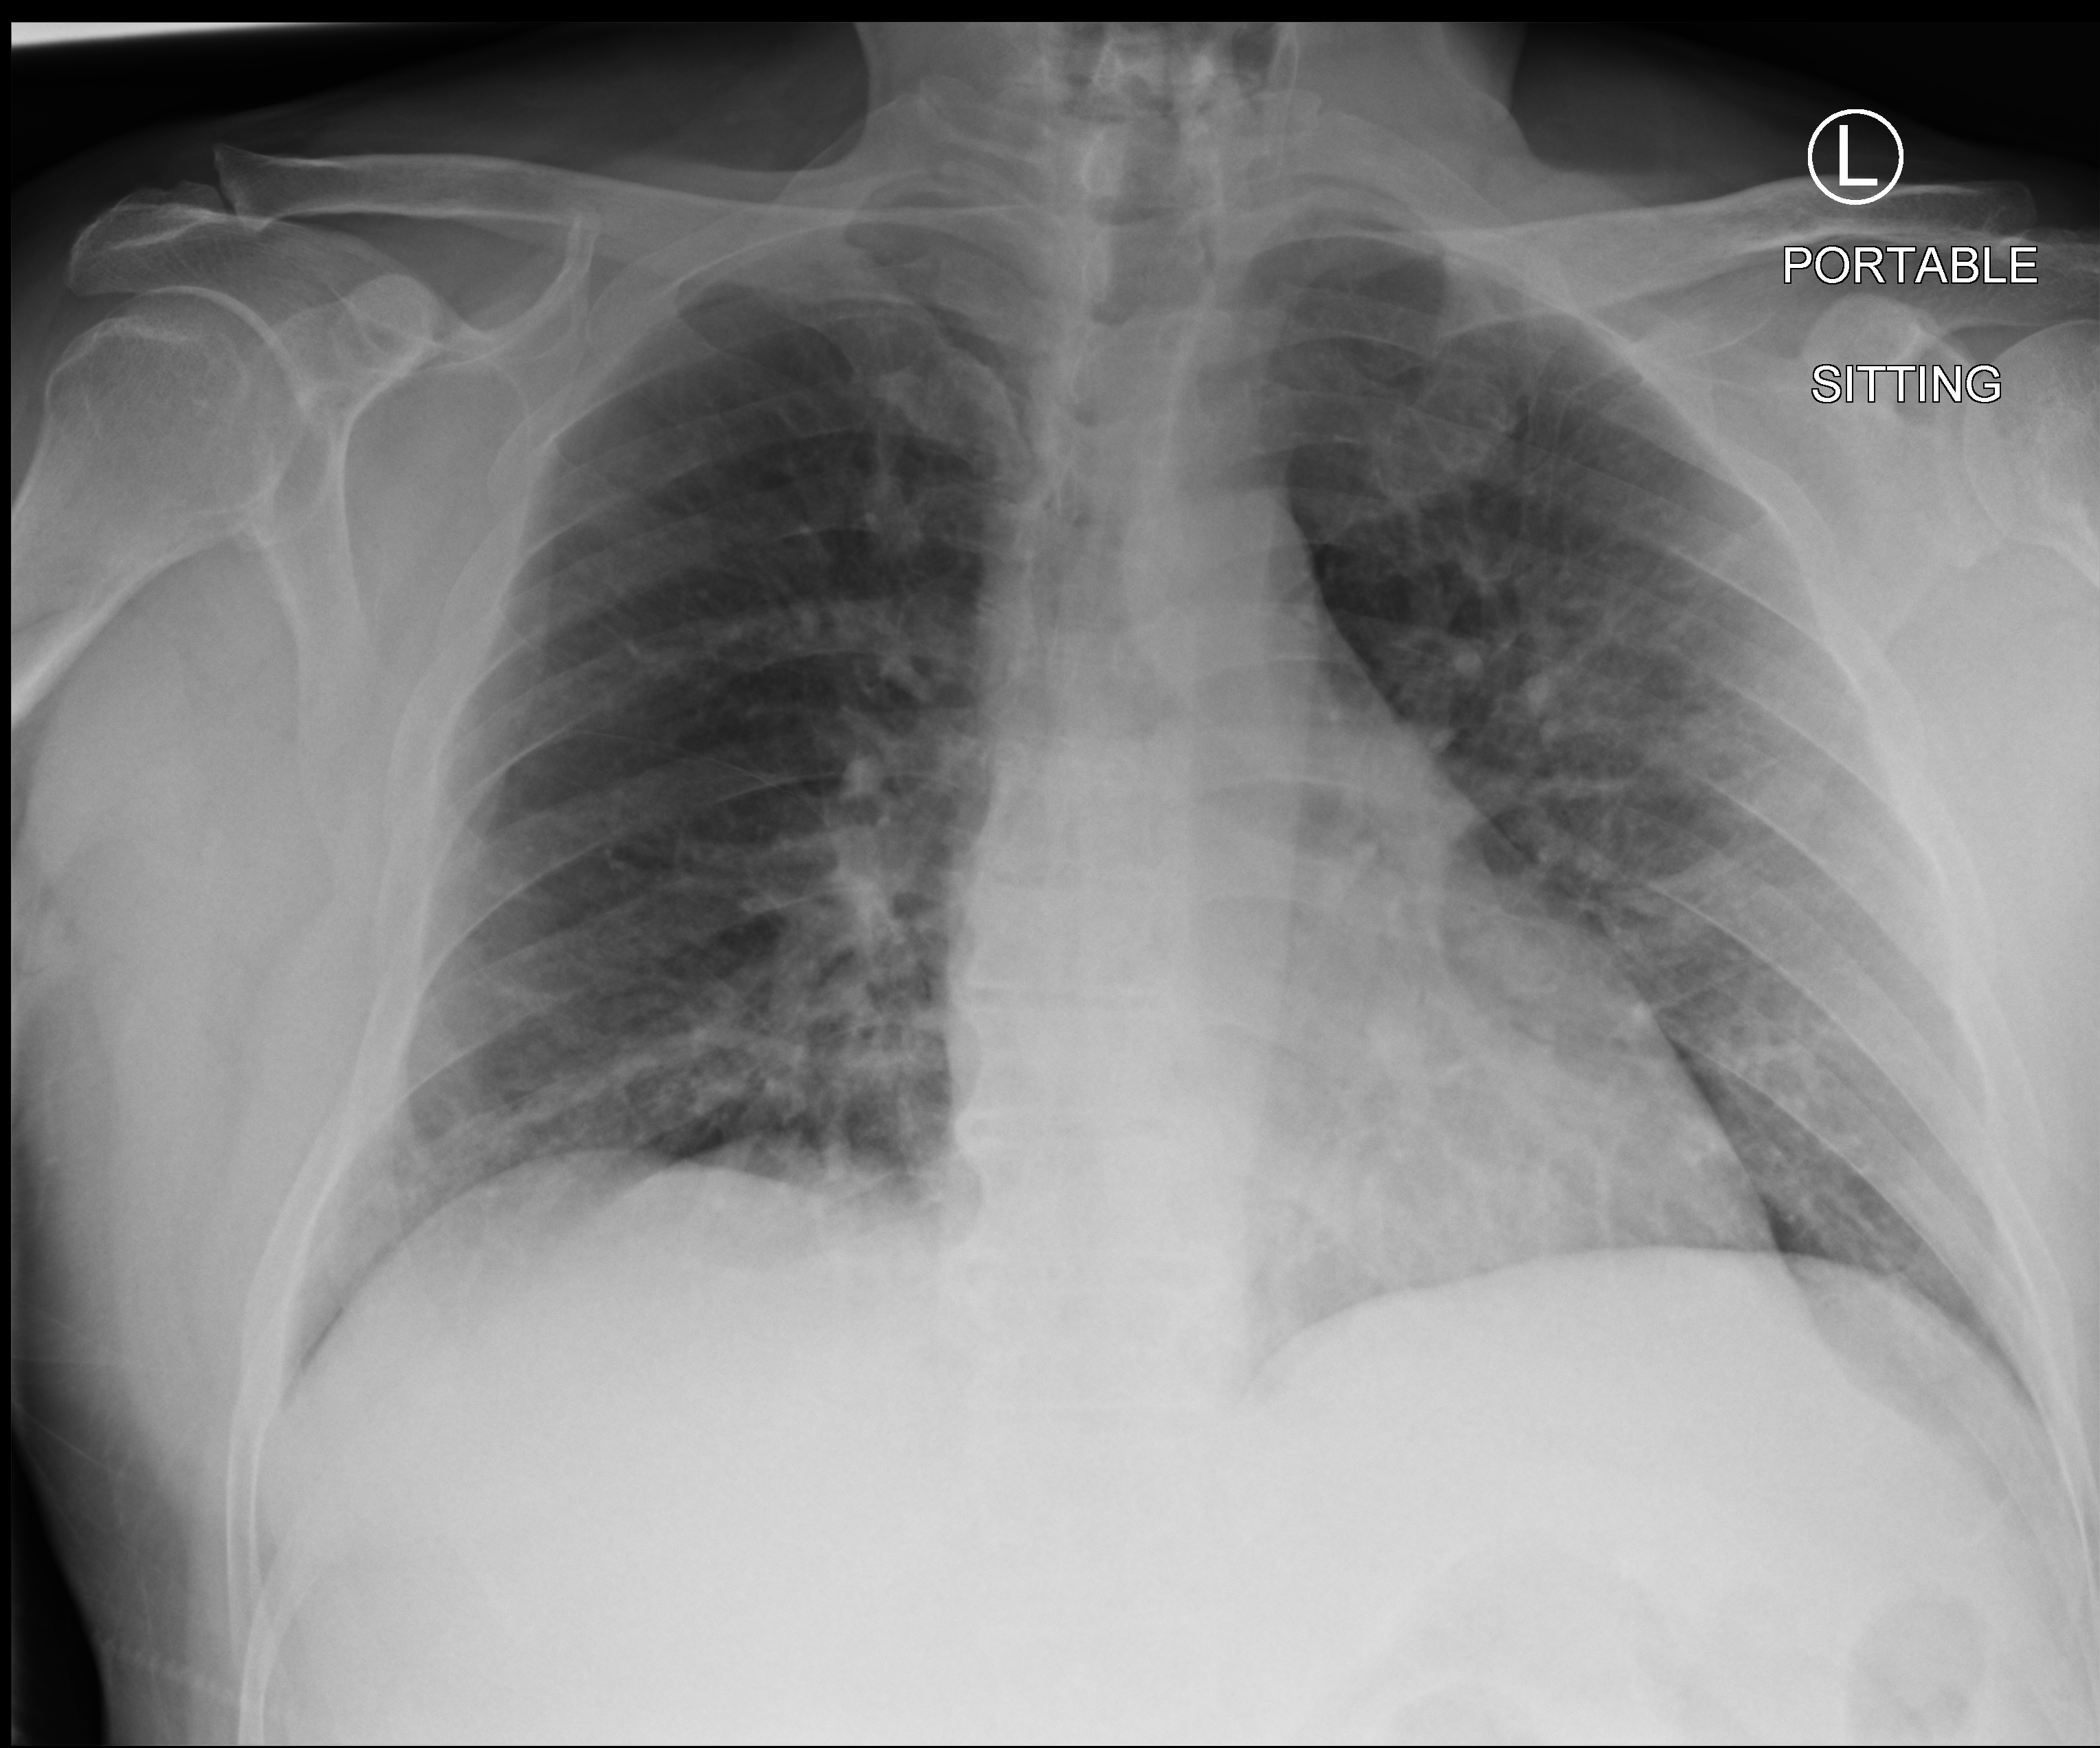
Portable chest radiograph, anteroposterior (AP) projection. Patient hospitalised with COVID-19; male, aged 18–59 years.
Hospital-stay facts (about this admission, not read from this image; timing relative to this image not recorded):
- mechanically ventilated during this hospital stay: no
- chronic kidney disease (admission record): no
- COPD (admission record): no